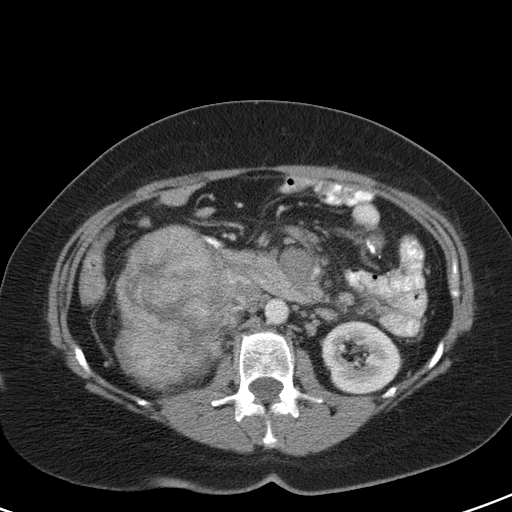
Contrast-enhanced abdominal CT, one axial slice; position 61 of 126 along the scan axis; soft-tissue window (W 400 / L 40 HU); 5 mm slice thickness; 512 × 512 image matrix, field of view 356 × 356 mm. Patient: female, 51 years. From the clinical record (not read from this slice): diagnosis: adrenocortical carcinoma; tumour side: right adrenal; tumour size at pathology: 17 cm; Ki-67 index: 12 %.
Structures marked on this image (semi-automatically segmented with operator editing):
- mass: bounding box [x1, y1, x2, y2] px = [118, 227, 229, 384]